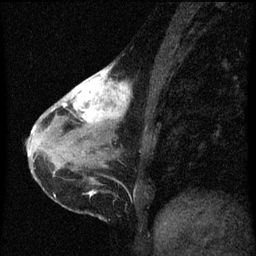
Breast MRI (dynamic contrast-enhanced), one sagittal slice. Slice 23 of 60 in the series (ordered by position). Dynamic contrast-enhanced series, image 2 of 3 at this slice position (ordered by acquisition). 1.5 T. TE 4.2 ms, TR 8 ms. 256 × 256 image matrix. Patient: female, 38 years.
Structures marked on this image (semi-automatic segmentation, software-assisted and operator-edited):
- analysis volume of interest (the breast-tissue region the enhancement analysis was run in; not a lesion): box from (x=61, y=64) to (x=131, y=147) px
- tumour enhancement mask (voxels above the 70 % enhancement threshold inside the analysis volume of interest): (x=61, y=66)–(x=131, y=123)